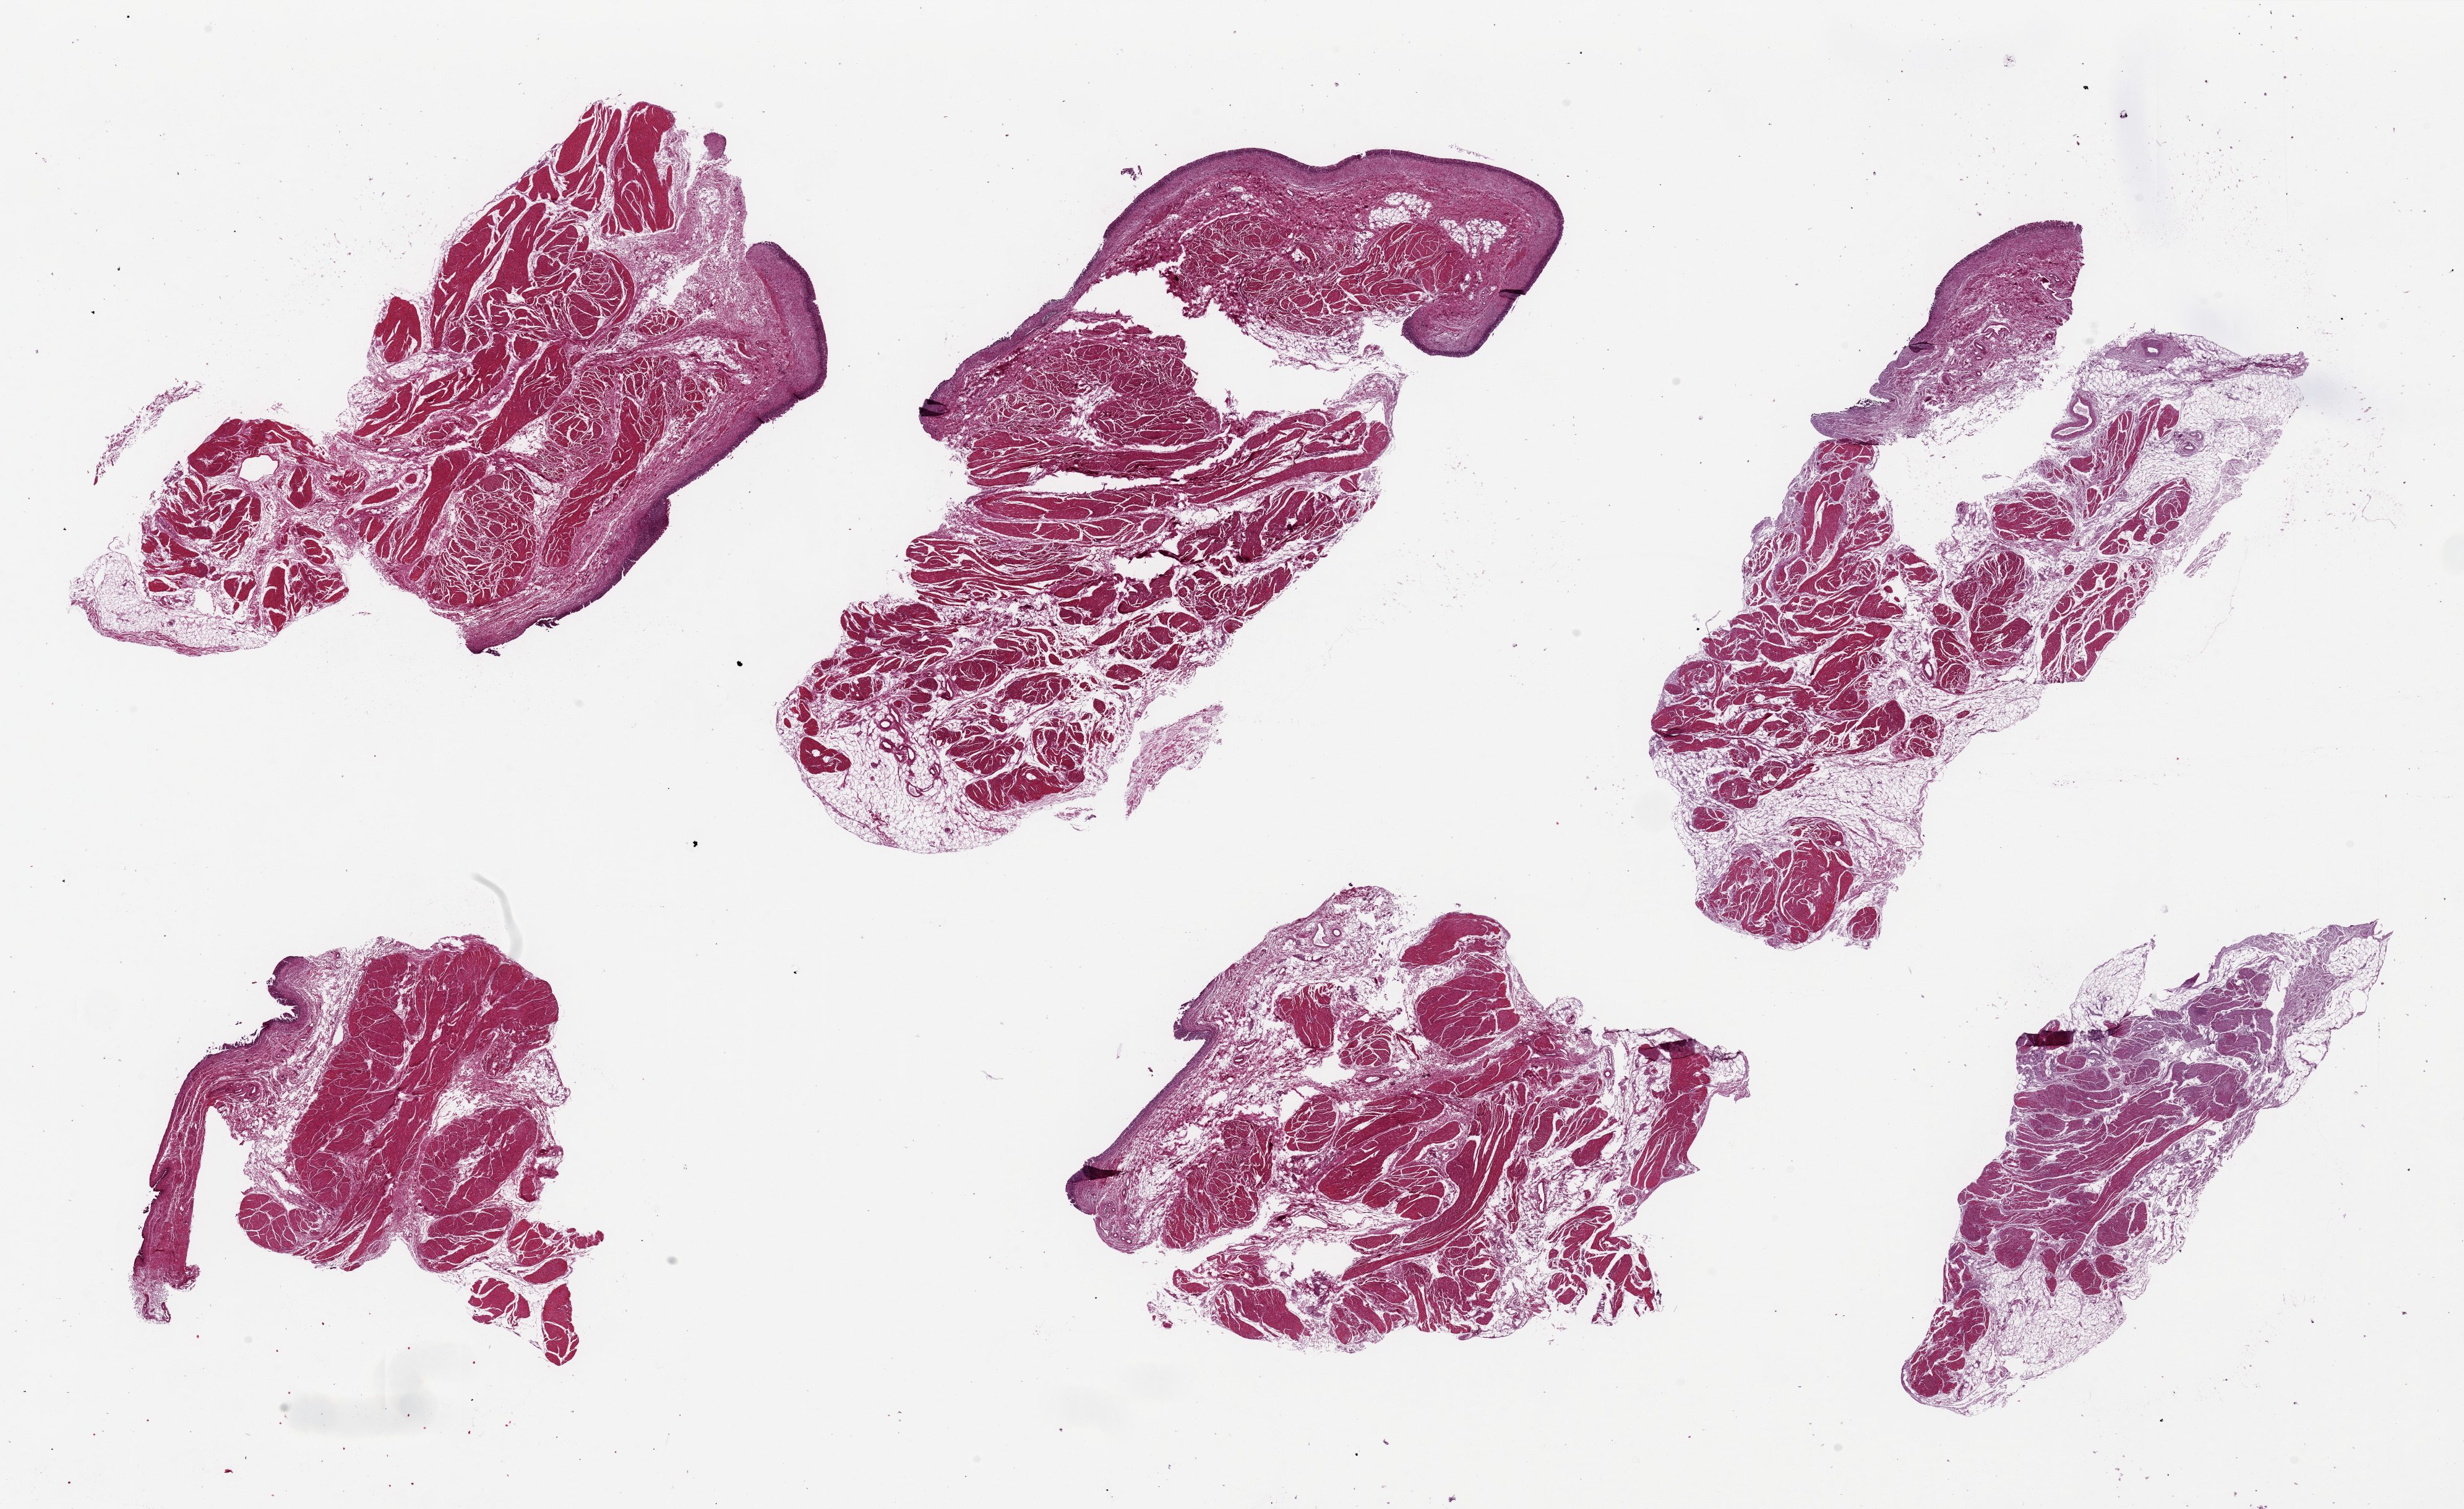
Digitized H&E-stained section — low-resolution overview of the scanned area, about 31.5 x 19.3 mm. PAXgene-fixed paraffin-embedded (PFPE) section. Section of urinary bladder (target tissue). Donor tissue sample. Donor sex: female.
- pathologist's review note for this sample: 6 pieces ~10x5mm, urothelium largely sloughed, where present less than 1% of thickness